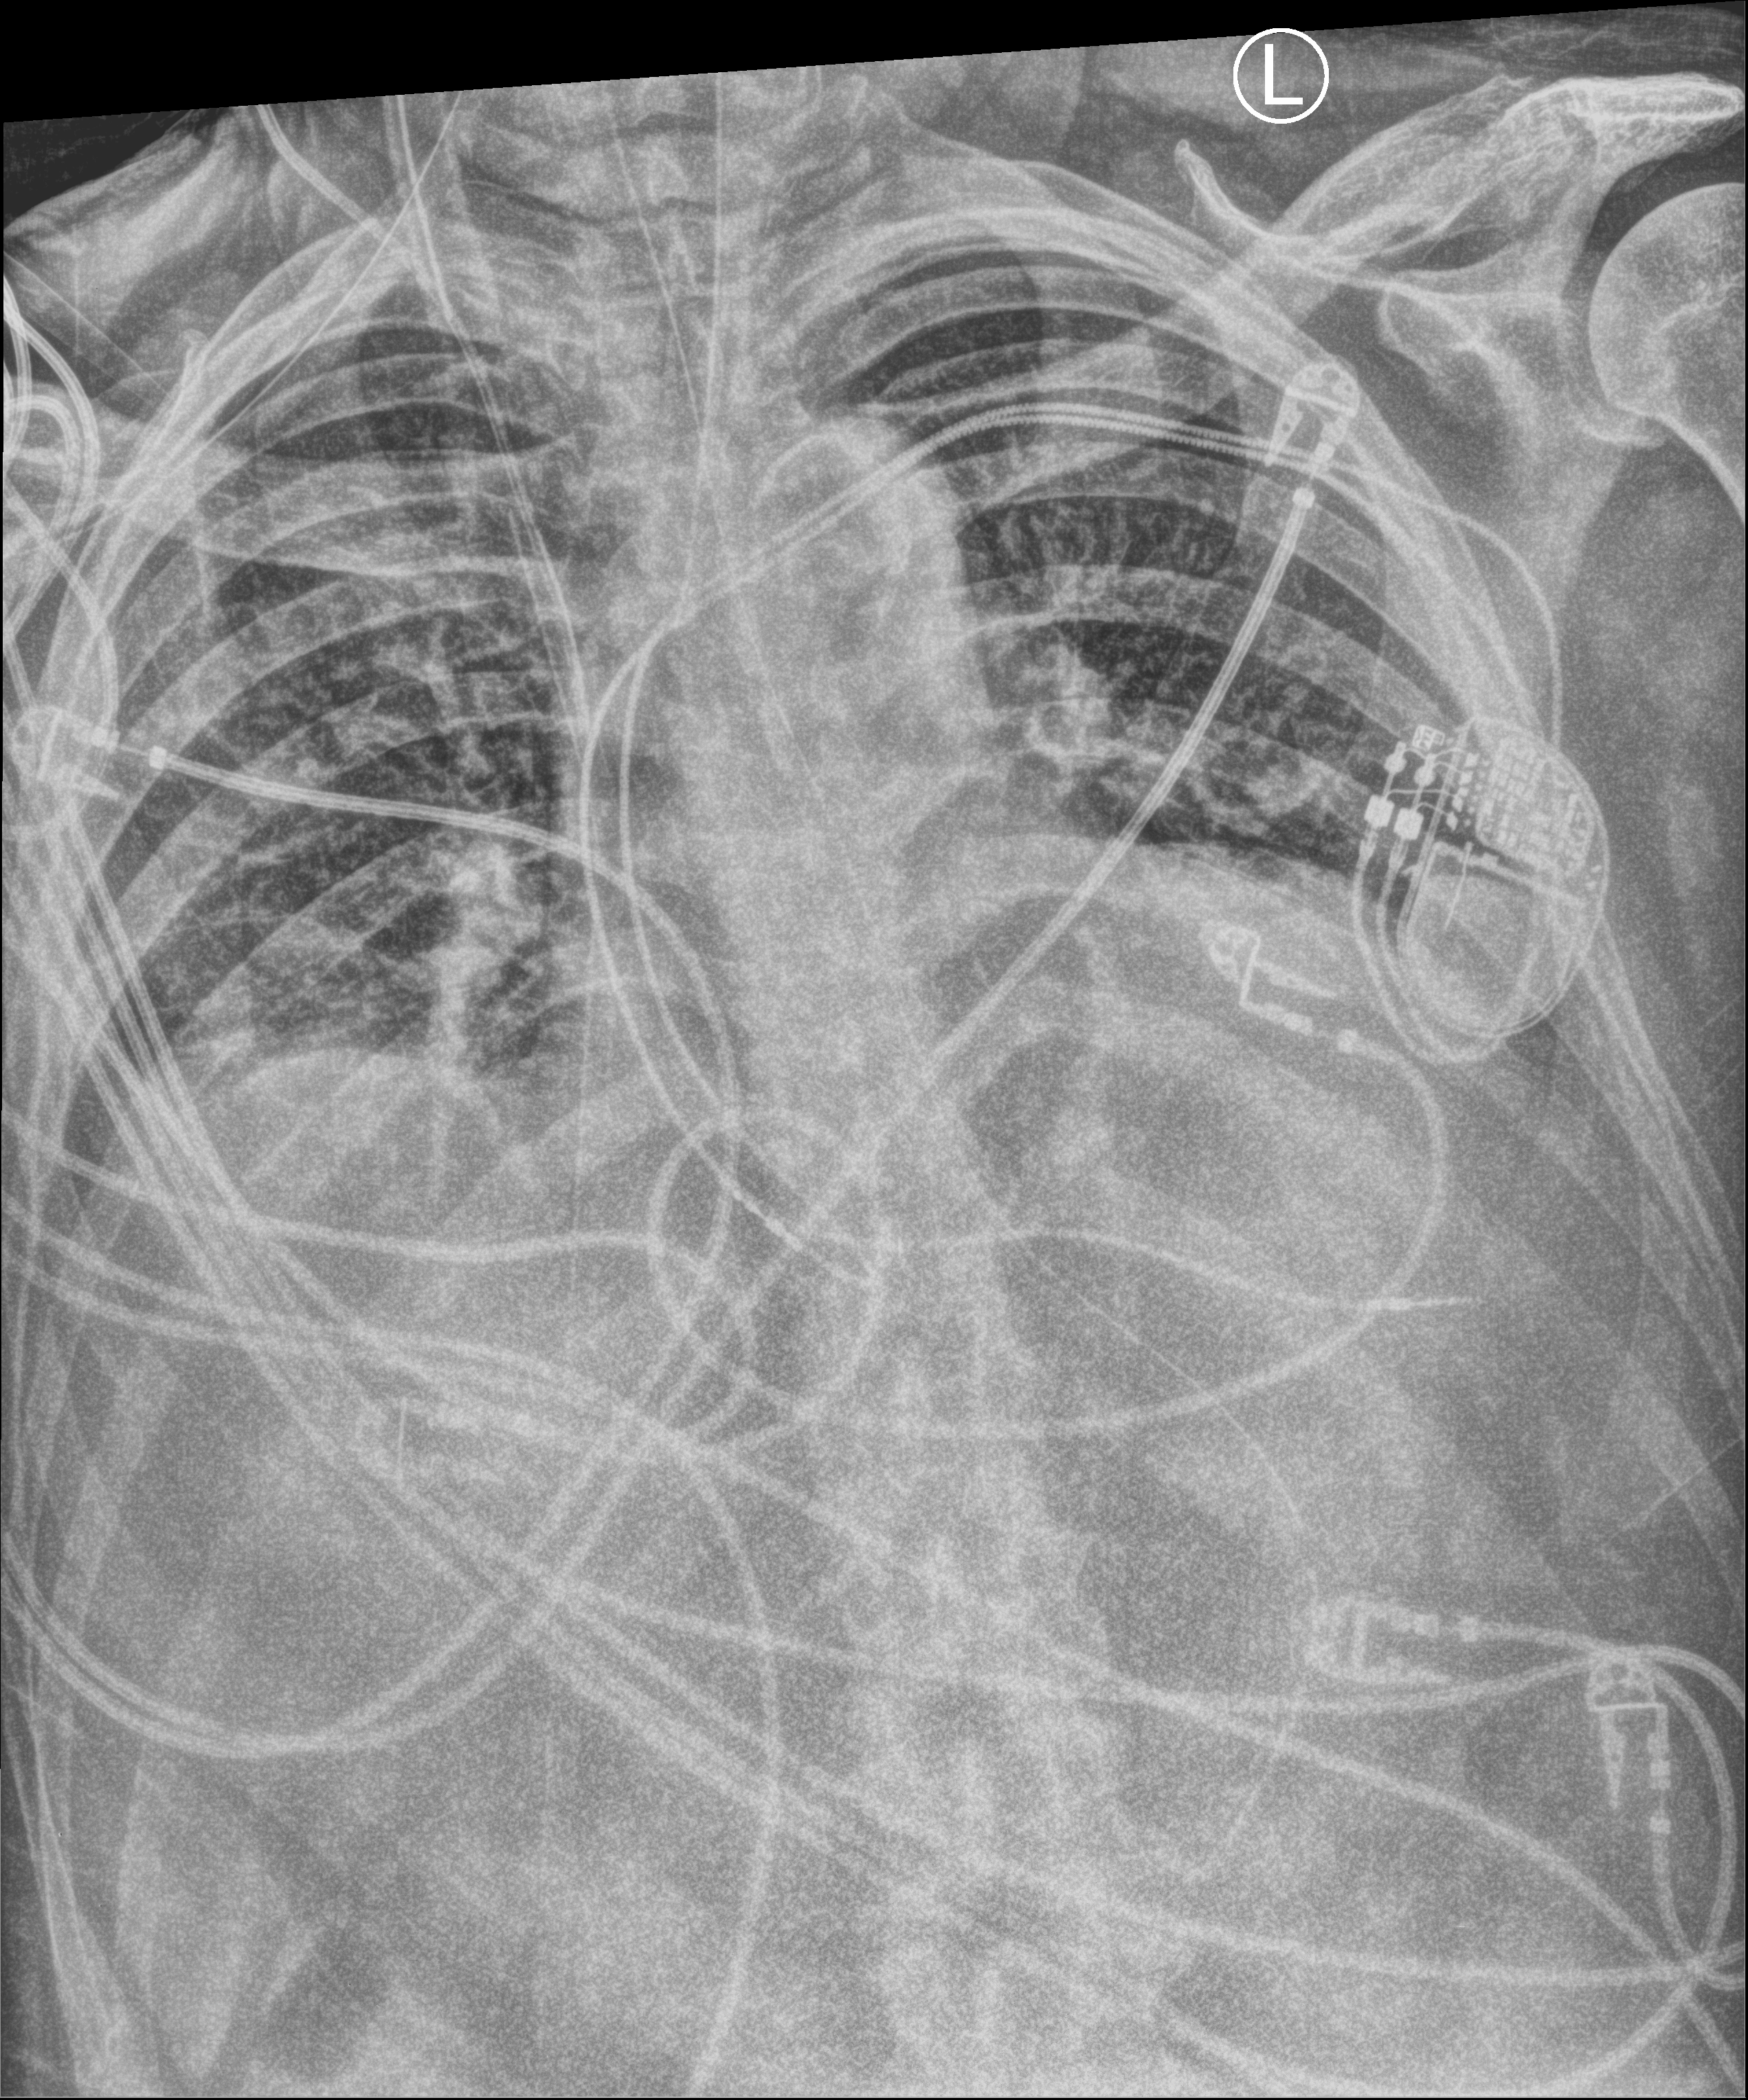
Chest X-ray (portable), anteroposterior (AP) projection. Male patient hospitalised with COVID-19, age 60–74 years.
From the hospital-stay record, not from the radiograph (when in the stay this image was taken is not recorded): admitted to intensive care during this hospital stay: yes.